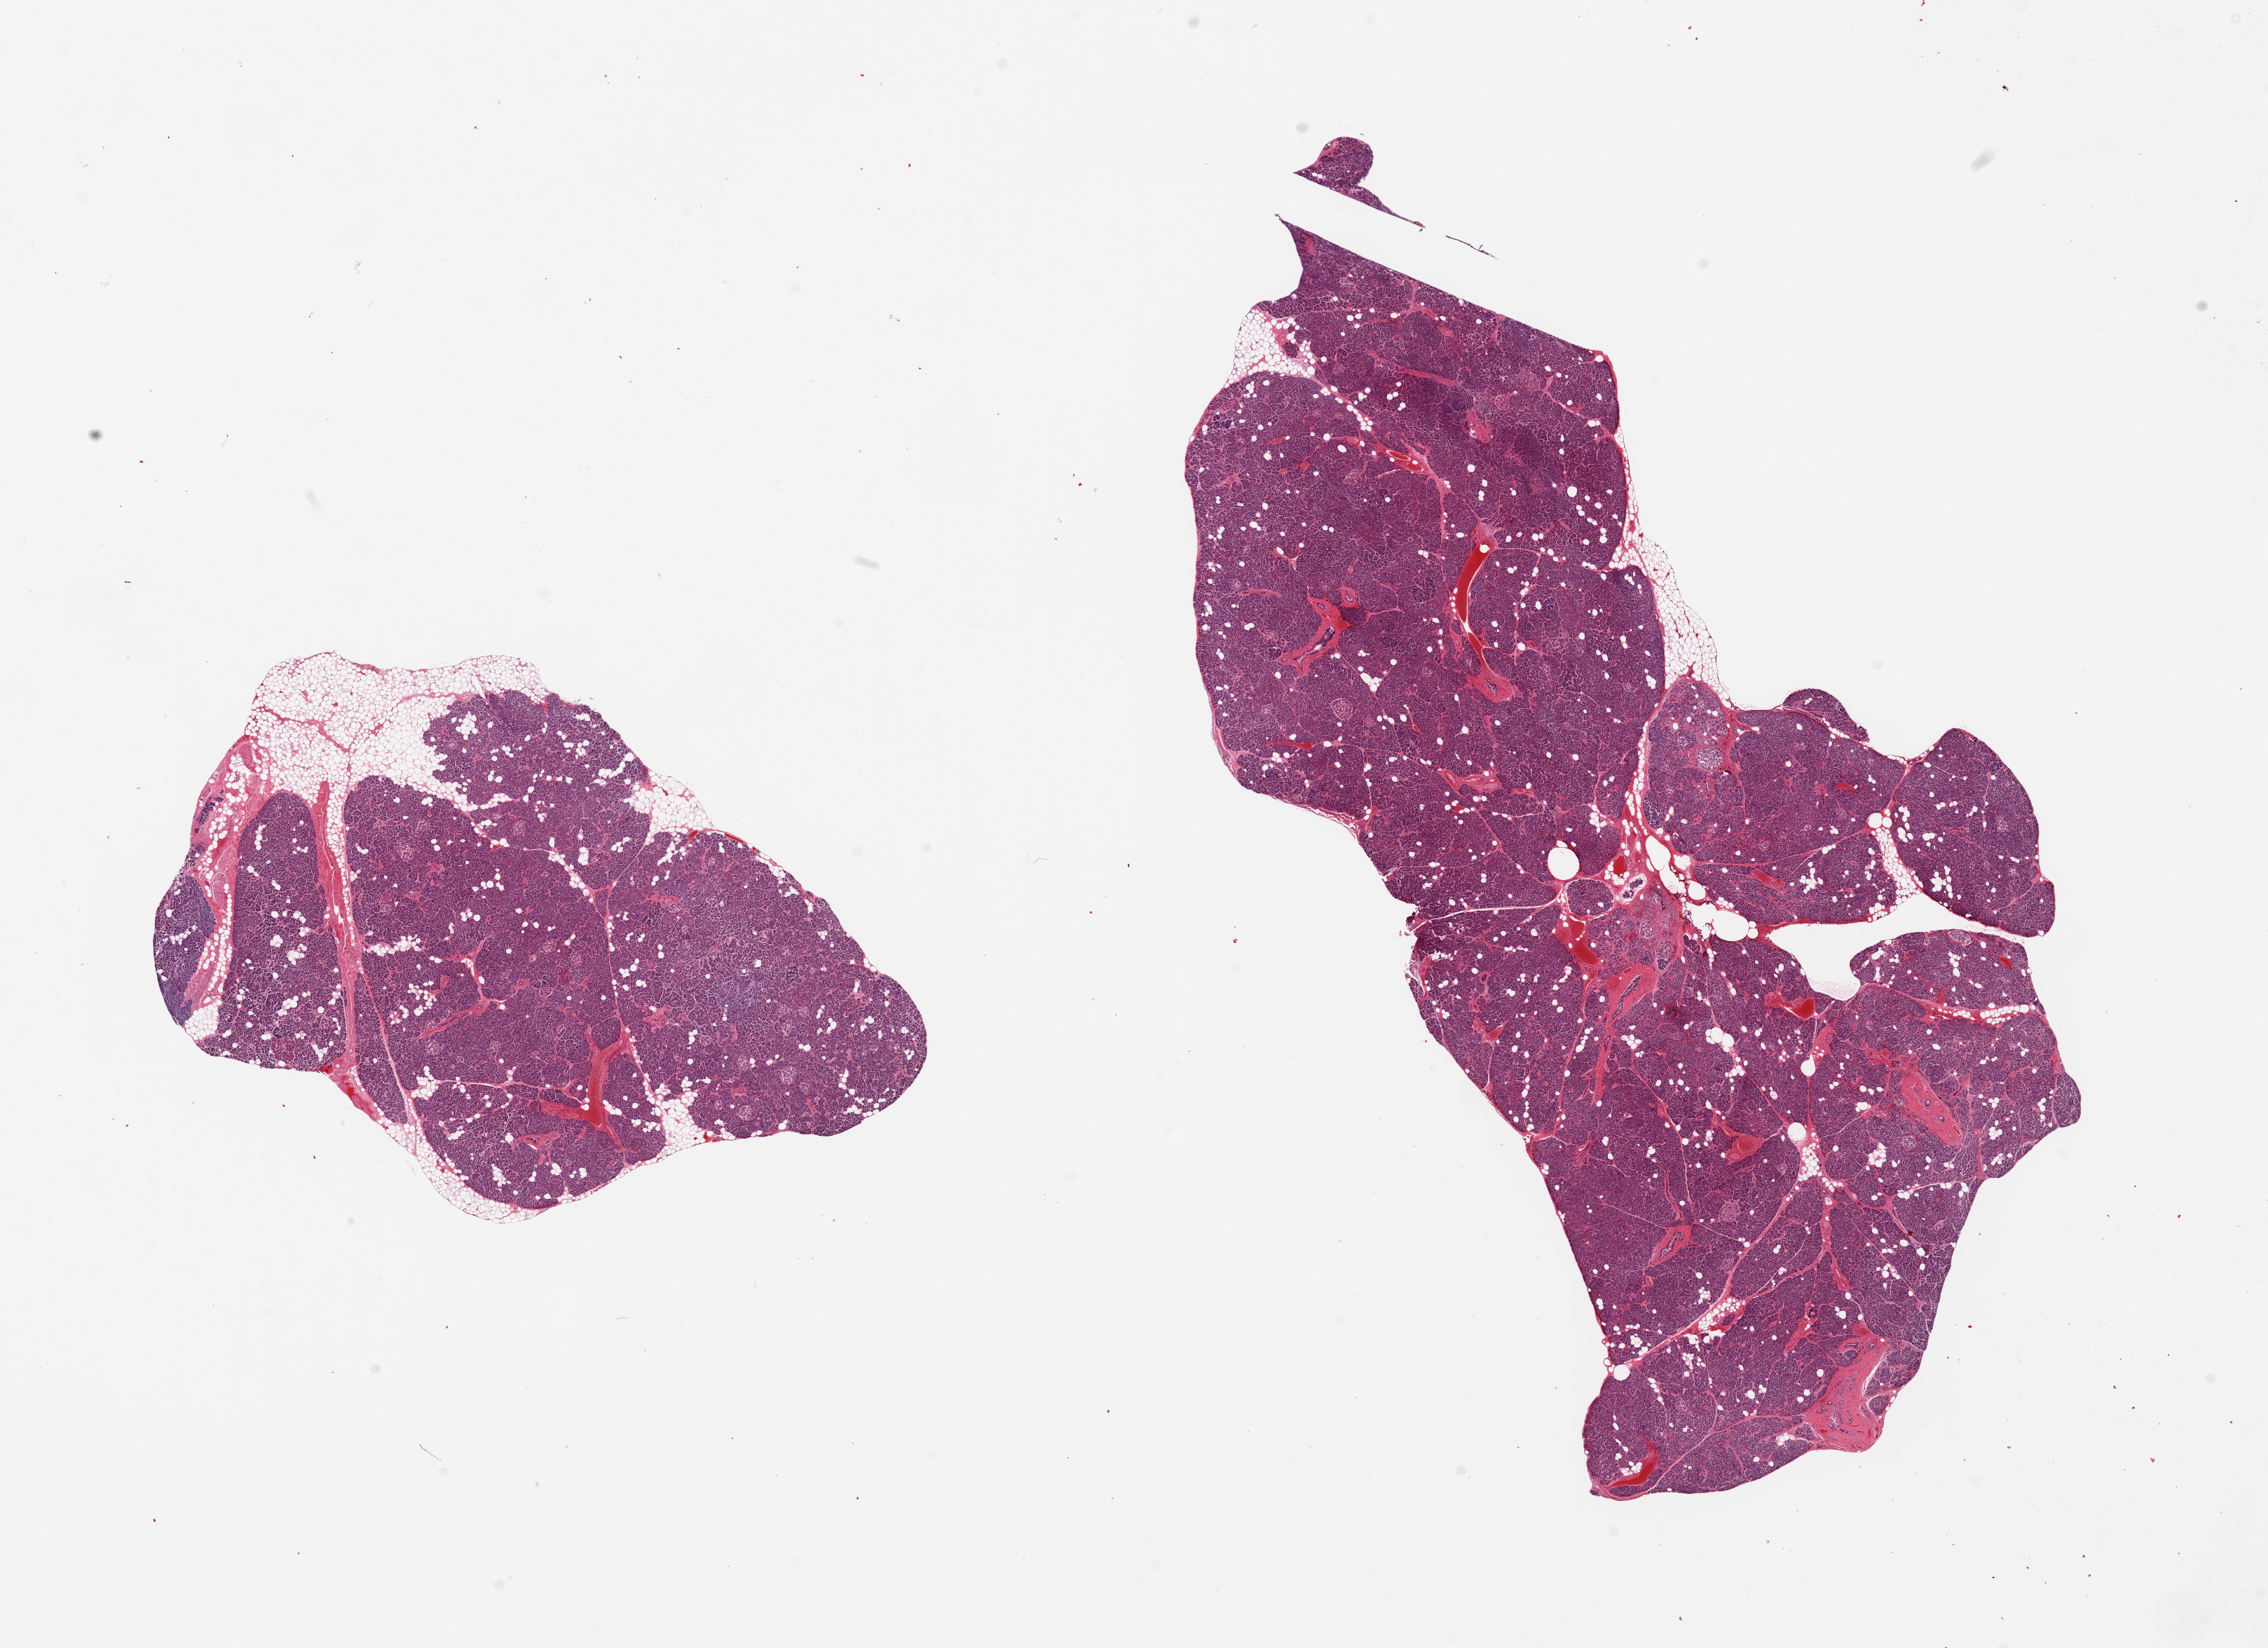
Whole-slide image, hematoxylin and eosin (H&E) stain, brightfield — whole scanned area (about 25.6 x 18.6 mm) shown as a low-resolution overview; PAXgene-fixed paraffin-embedded (PFPE) section; target tissue: pancreas; tissue donor sample. Donor sex: male.
• reviewer comment on this tissue sample: 2 pieces; one piece with 10-20% attached fat and nerve, mild to moderate autolysis, islets well visualized